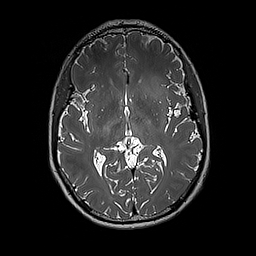
Brain MRI from a brain-tumour surgery series, one axial slice. Slice 101 of 192 in the series (ordered by position). 1 mm slice thickness. 256 × 256 image matrix, field of view 250 × 250 mm. From the clinical record (not read from this slice): histopathology: Glioblastoma; WHO grade: 4; IDH mutation: no.
Structures marked on this image (manually delineated by an expert):
- tumour: box from (x=140, y=76) to (x=171, y=113) px